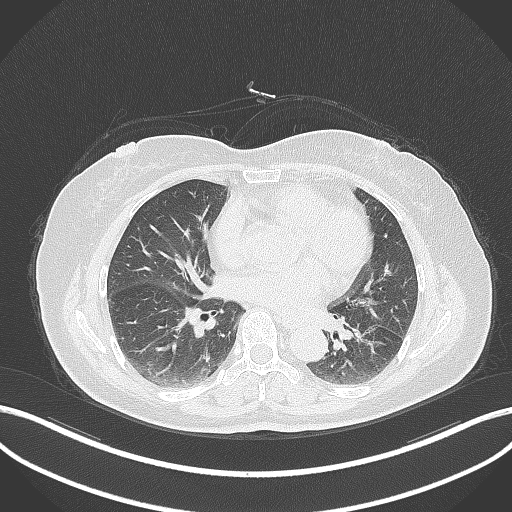
Chest CT, one axial slice. Slice 172 of 311 in the series (ordered by position). Lung window (W 1500 / L -600 HU). 512 × 512 image matrix, field of view 400 × 400 mm. Female patient, age 59 years. From the clinical record (not read from this slice): clinical TNM (as recorded): T2a N0 M0; histopathological grade: G2-3.
Annotated regions visible in this slice (bounding box drawn by a radiologist):
- lung tumour (recorded histology: adenocarcinoma): bounding box (x1, y1, x2, y2) in pixels: (351, 322, 387, 355)